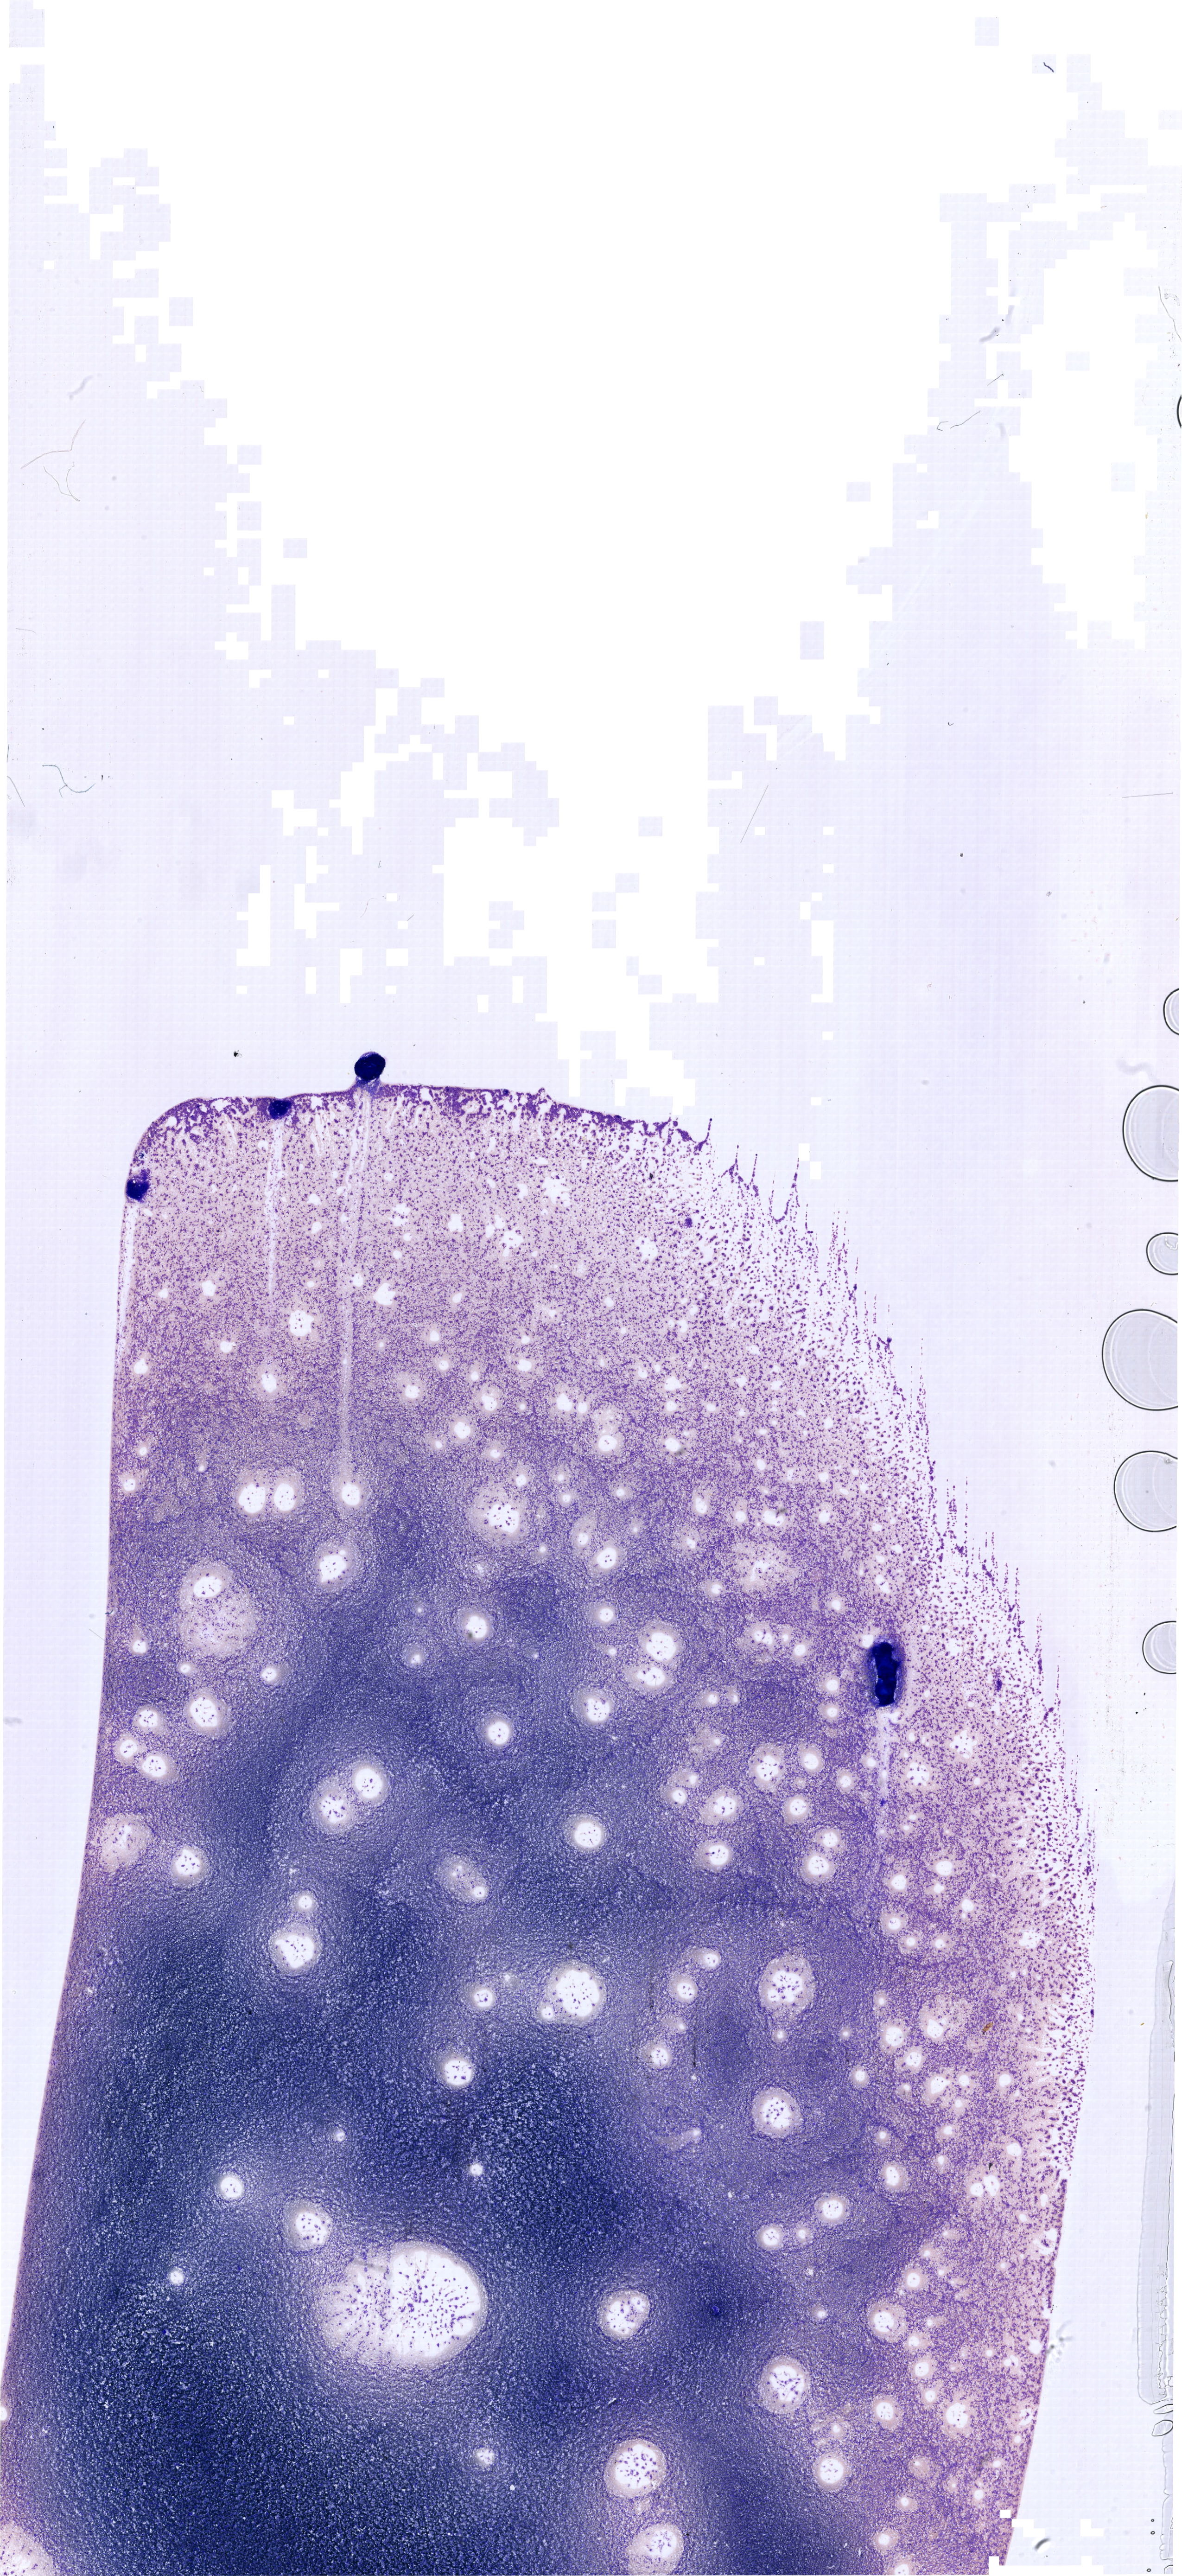
Bone marrow aspirate smear, May-Grünwald-Giemsa (MGG) stain, whole-slide image — shown as a low-resolution overview of the whole scanned area (about 19.9 x 43.4 mm). Patient sex: male.
* diagnosis: Mixed Phenotype Acute Leukemia, B/Myeloid